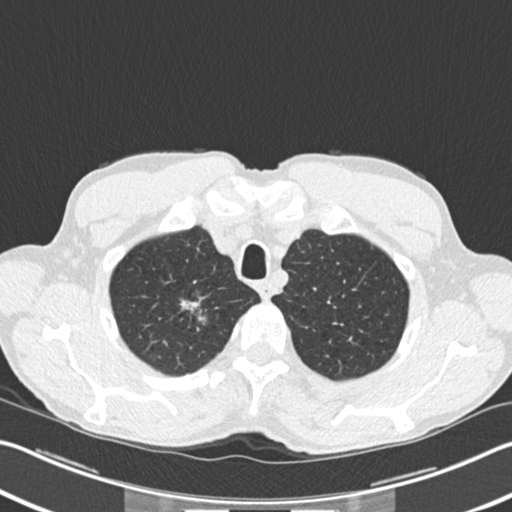
Low-dose screening chest CT, one axial slice; position 190 of 220 along the scan axis; 120 kVp; lung window (W 1500 / L -600 HU); 512 × 512 image matrix.
Annotated regions visible in this slice (expert manual segmentation):
- lesion 1 (tumor, upper lobe of right lung): box from (x=181, y=300) to (x=206, y=324) px